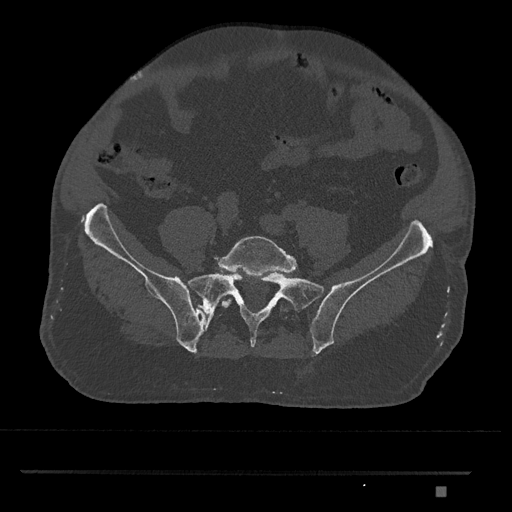
CT including the spine, one axial slice; position 523 of 1134 along the scan axis; reconstruction kernel Br40s/3; bone window (W 1800 / L 400 HU); 0.5 mm slice thickness; 512 × 512 image matrix, field of view 429 × 429 mm. Patient: male, 65 years. From the clinical record (not read from this slice): primary cancer: prostate.
Annotated regions visible in this slice (semi-automatically segmented with operator editing):
- L5 vertebra: bounding box [x1, y1, x2, y2] px = [216, 236, 297, 309]